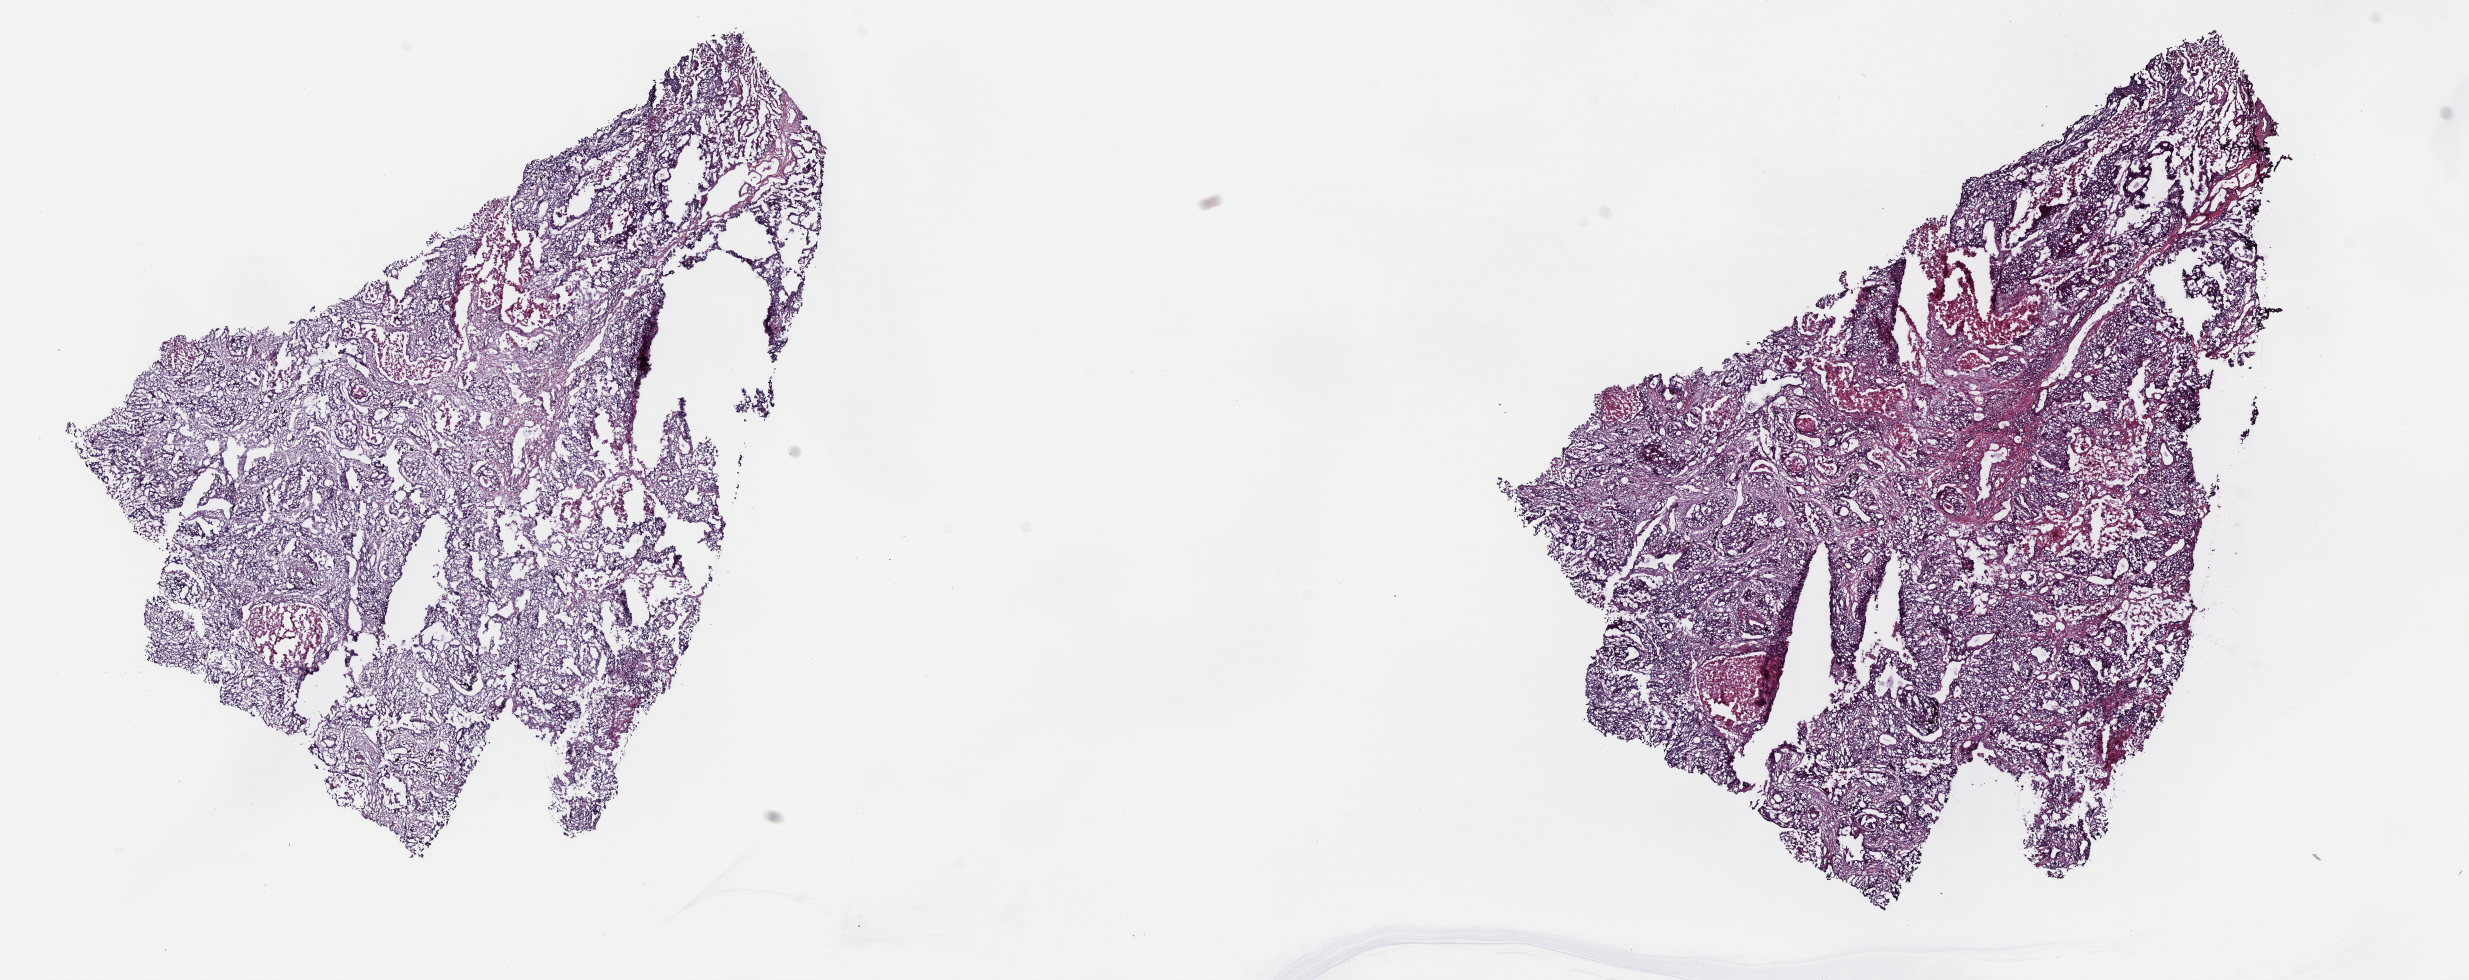
Digitized H&E tissue section (whole slide), whole scanned area (about 19.5 x 7.7 mm, from a 40x scan) shown as a low-resolution overview. Frozen section from the top of the tissue portion. Lung, primary tumour sample. Male, age 77 years at initial diagnosis. Slide review estimates, as recorded: tumour cells 50%, tumour nuclei 60%, normal cells 10%, stromal cells 30%, necrosis 10%. Infiltration values recorded for this section: lymphocyte infiltration 5%, monocyte infiltration 5%, neutrophil infiltration 0%.
Laterality: right. AJCC pathologic stage: IB. Histologic diagnosis: Squamous cell carcinoma, NOS (upper lobe, lung).